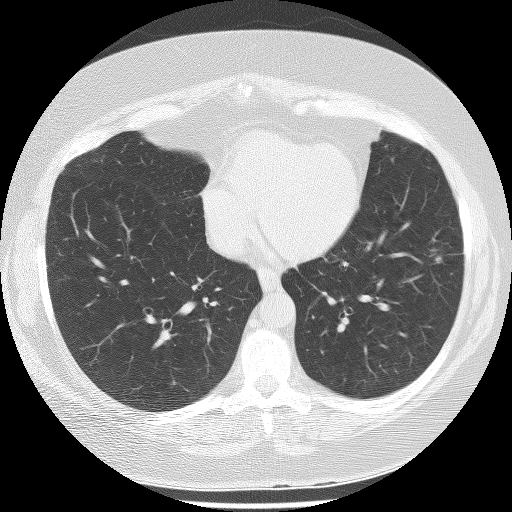
Low-dose screening chest CT, one axial slice. Slice 97 of 233 in the series (ordered by position). Reconstruction kernel BONE. 120 kVp. Lung window (W 1500 / L -600 HU). 2.5 mm slice thickness. 512 × 512 image matrix, field of view 340 × 340 mm.
Structures marked on this image (manually delineated by an expert):
- lesion 1 (tumor, lower lobe of left lung): box from (x=436, y=256) to (x=441, y=263) px